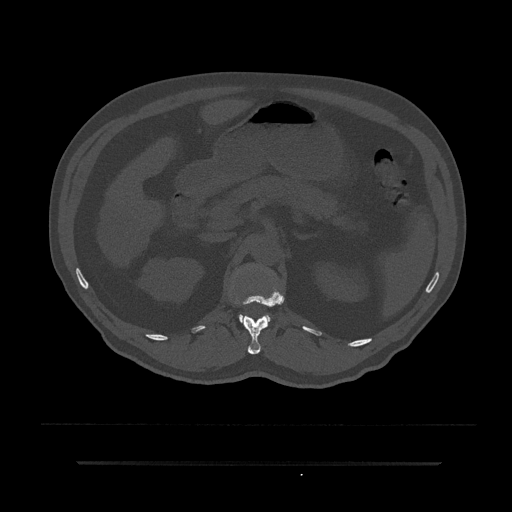
CT including the spine, one axial slice. Slice 185 of 797 in the series (ordered by position). Reconstruction kernel Br40s/3. Bone window (W 1800 / L 400 HU). 0.5 mm slice thickness. 512 × 512 image matrix. Male patient, age 59 years. From the clinical record (not read from this slice): primary cancer: bile ducts.
Structures marked on this image (semi-automatic segmentation, software-assisted and operator-edited):
- L1 vertebra: box from (x=238, y=300) to (x=270, y=322) px
- T12 vertebra: (x=233, y=286)–(x=284, y=355)